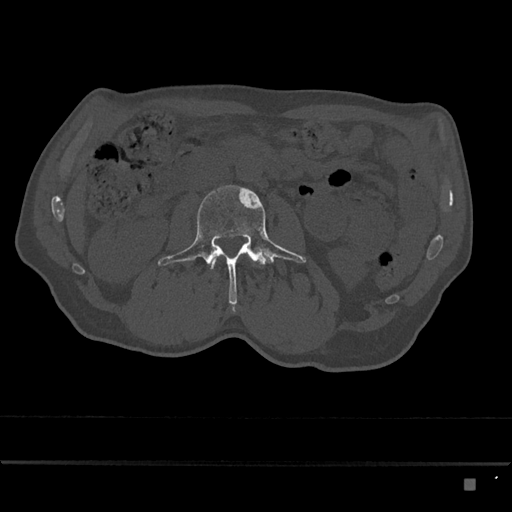
CT including the spine, one axial slice; slice 416 of 797 in the series (ordered by position); reconstruction kernel Br40s/3; bone window (W 1800 / L 400 HU); 512 × 512 image matrix. Male patient, age 72 years. Case-level facts recorded for this patient, not image findings: primary cancer: prostate.
Outlined on this slice (semi-automatic segmentation, software-assisted and operator-edited):
- L2 vertebra: box from (x=211, y=256) to (x=219, y=270) px
- L3 vertebra: (x=158, y=185)–(x=306, y=312)